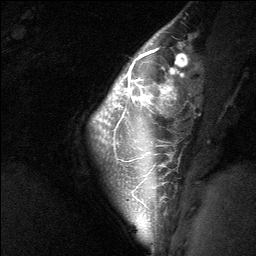
Breast MRI (dynamic contrast-enhanced), one sagittal slice; slice 50 of 64 in the series (ordered by position); dynamic contrast-enhanced study with each time point stored as its own series, time point 2 of 3 at this slice position (early post-contrast, ordered by acquisition time); 1.5 T; TE 4.8 ms, TR 27 ms; 2 mm slice thickness; 256 × 256 image matrix, field of view 180 × 180 mm. Female patient, age 26 years. Case-level facts recorded for this patient, not image findings: setting: breast cancer imaged before/during neoadjuvant chemotherapy; receptor status: HR-positive, HER2-negative.
Structures marked on this image (semi-automatic segmentation, software-assisted and operator-edited):
- analysis volume of interest (the breast-tissue region the enhancement analysis was run in; not a lesion): bounding box [x1, y1, x2, y2] px = [90, 43, 182, 138]
- tumour enhancement mask (voxels above the 90 % enhancement threshold inside the analysis volume of interest): [127, 49, 175, 101]